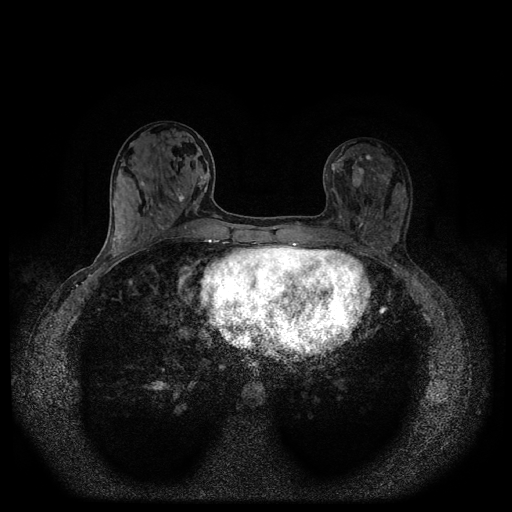
Breast MRI (dynamic contrast-enhanced, multi-phase), one axial slice; dynamic contrast-enhanced series, time point 2 of 5 at this slice position (early post-contrast); 1.5 T; TE 2.6 ms, TR 5.4 ms; 2 mm slice thickness; 512 × 512 image matrix, field of view 340 × 340 mm. Female patient, age 32 years.
Annotated regions visible in this slice (semi-automatic segmentation, software-assisted and operator-edited):
- breast lesion (labelled benign in the annotation): bounding box (x1, y1, x2, y2) in pixels: (349, 166, 364, 190)